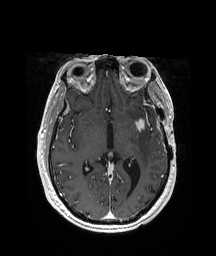
Brain MRI from a brain-tumour surgery series, one axial slice. T1-weighted post-contrast. 216 × 256 image matrix, field of view 228 × 270 mm. Case-level facts recorded for this patient, not image findings: histopathology: Glioblastoma; WHO grade: 4; IDH mutation: no.
Structures marked on this image (expert manual segmentation):
- tumour: bounding box [x1, y1, x2, y2] px = [143, 119, 153, 131]